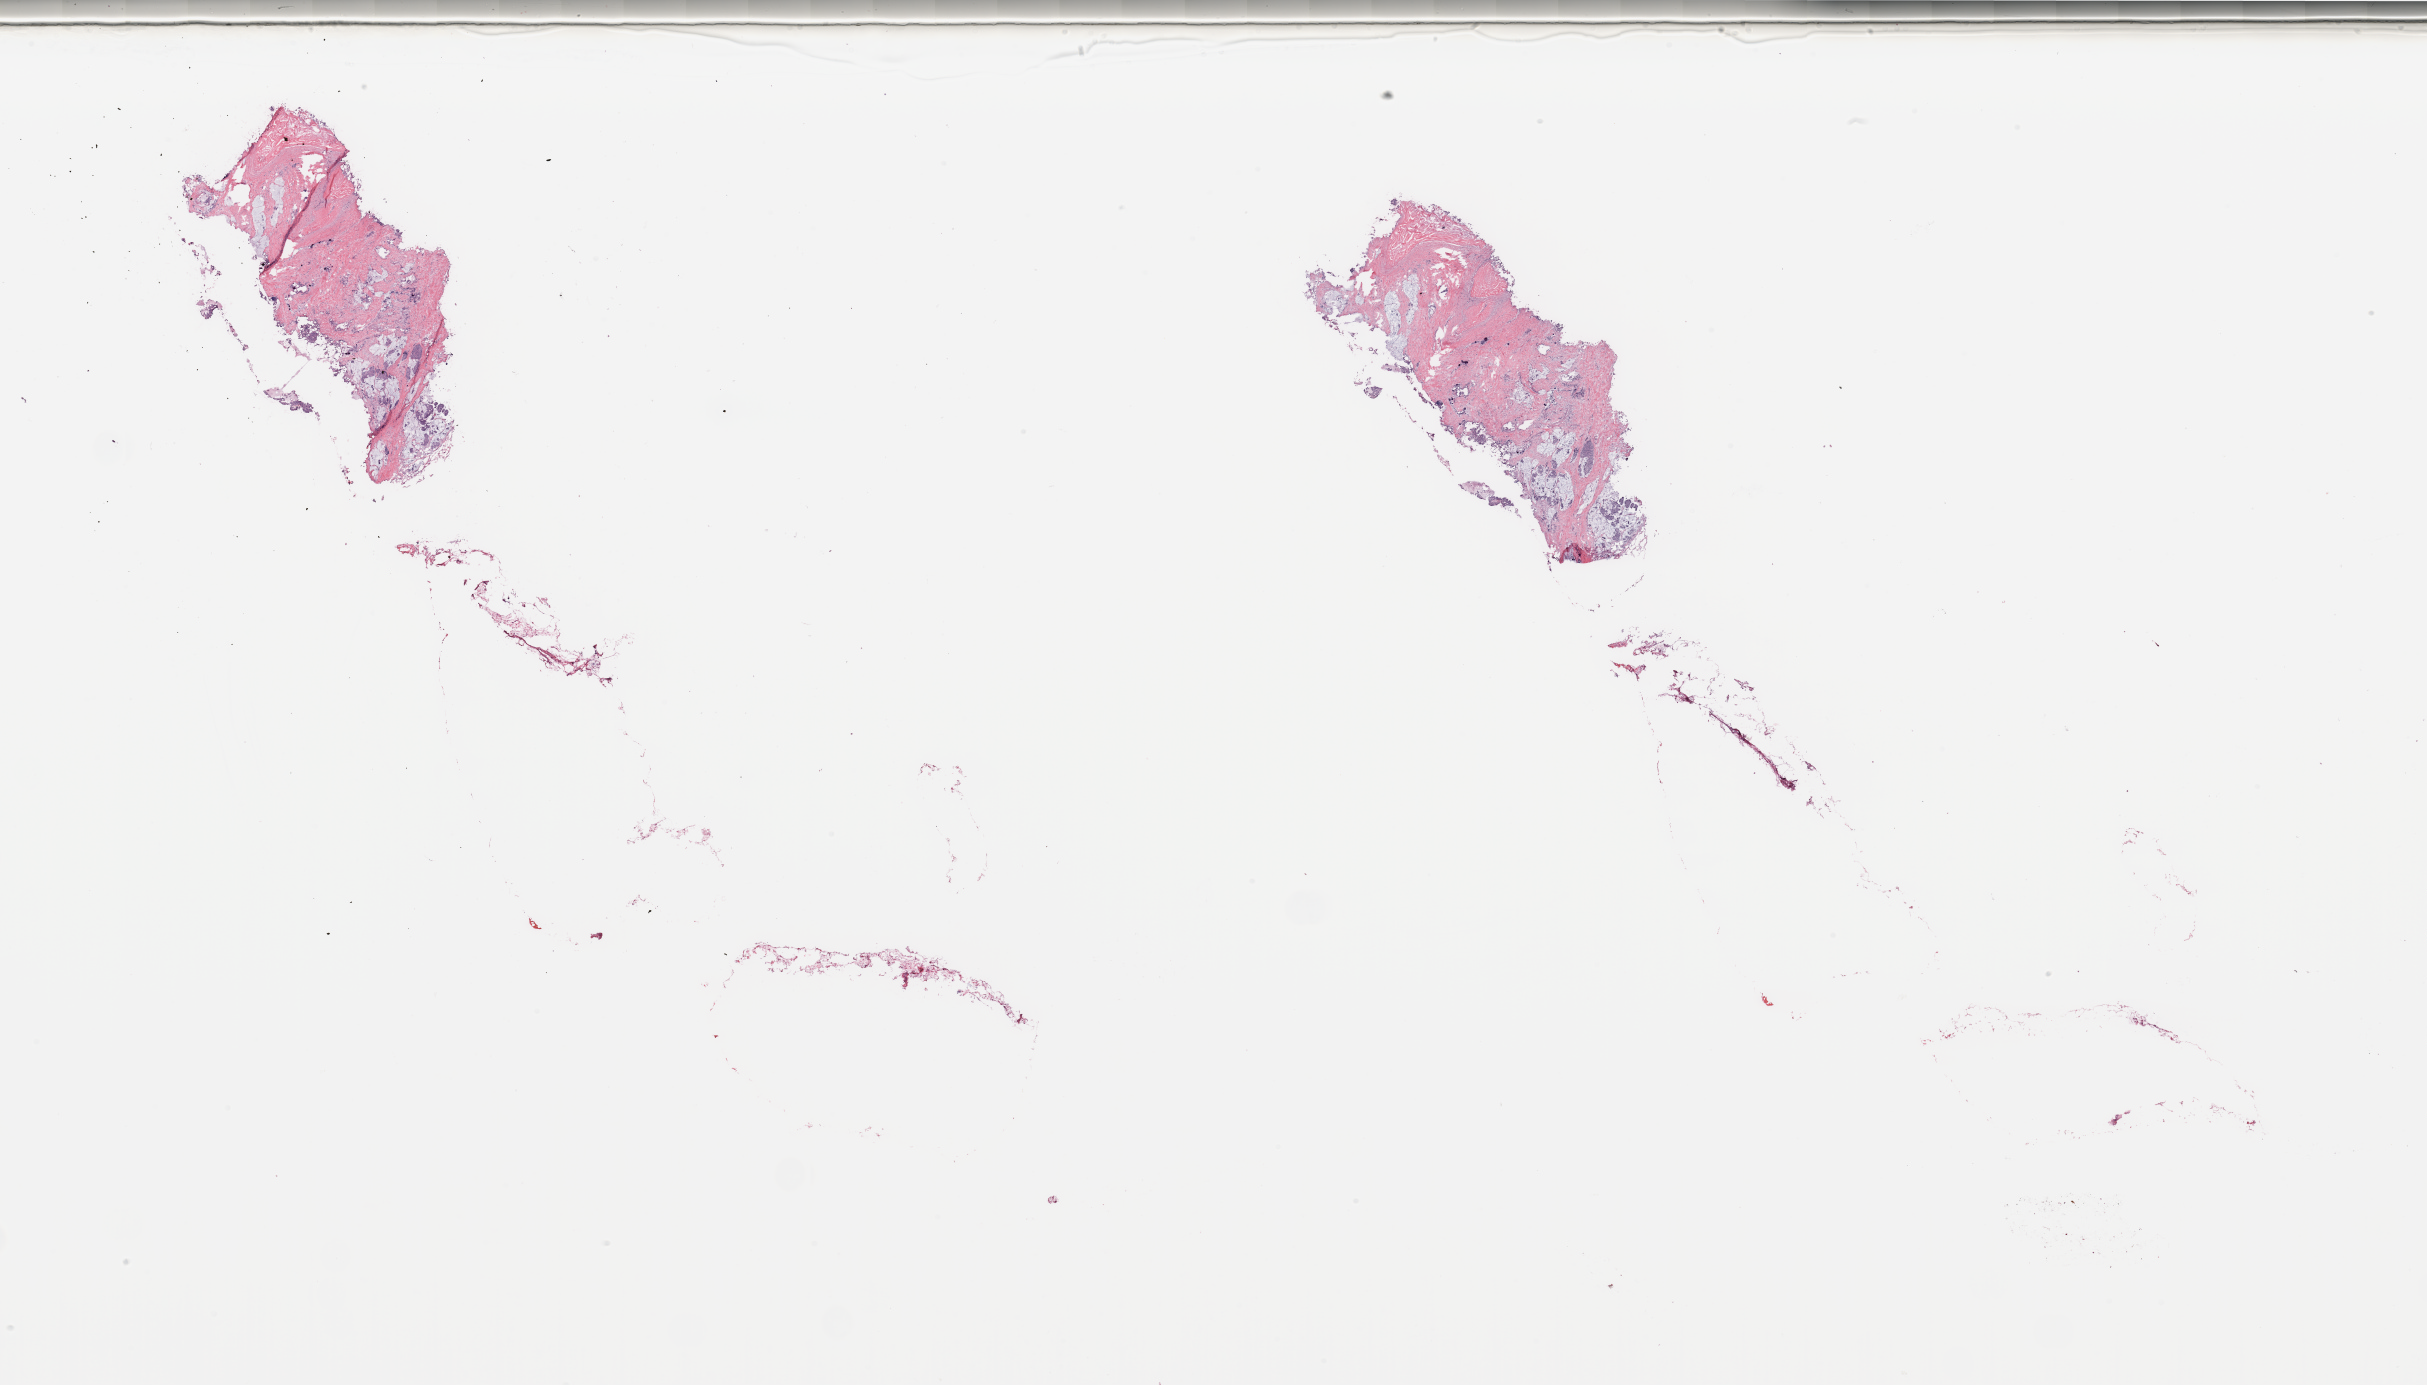
Digitized H&E tissue section (whole slide) — low-resolution overview of the scanned area, about 38.4 x 21.9 mm (from a 20x scan); breast, tissue type not recorded.
Patient diagnosis (cohort enrolment): breast cancer (breast).